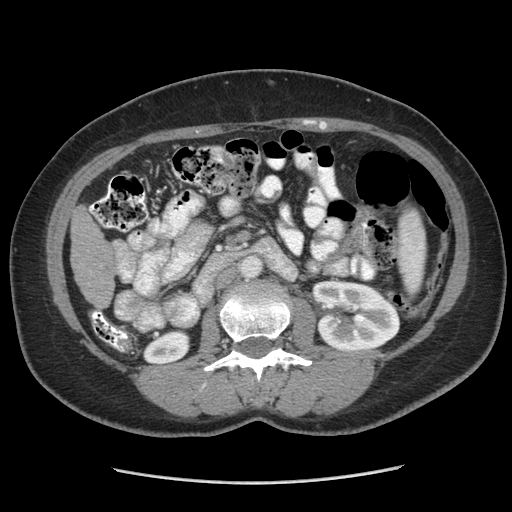
Contrast-enhanced abdominal CT (liver protocol), one axial slice. Position 117 of 185 along the scan axis. Soft-tissue window (W 400 / L 40 HU). 2.5 mm slice thickness. 512 × 512 image matrix, field of view 360 × 360 mm. Case-level facts recorded for this patient, not image findings: diagnosis: hepatocellular carcinoma (patient treated with transarterial chemoembolisation; whether this scan precedes or follows treatment is not stated here); TNM stage (as recorded): Stage-I; Child-Pugh class: A.
Annotated regions visible in this slice (semi-automatically segmented with operator editing):
- liver parenchyma outside the tumour (the mass and vessels are separate outlines, so this box may not span the whole liver): bounding box <70,206,114,306> (left, top, right, bottom; pixels)